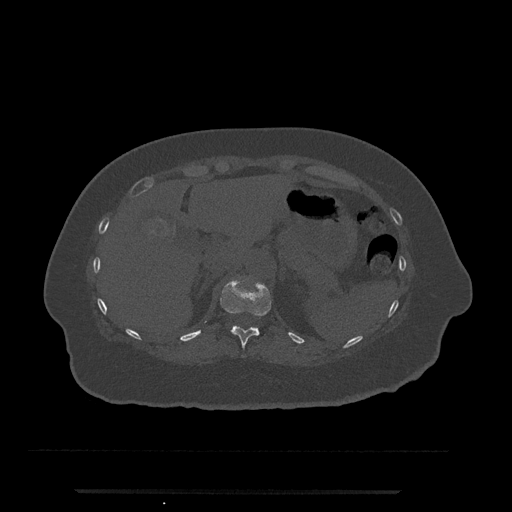
CT including the spine, one axial slice. Slice 218 of 797 in the series (ordered by position). Reconstruction kernel Br40s/3. Bone window (W 1800 / L 400 HU). 512 × 512 image matrix, field of view 440 × 440 mm. Female patient, age 51 years. From the clinical record (not read from this slice): primary cancer: neuro.
Outlined on this slice (semi-automatic segmentation, software-assisted and operator-edited):
- T11 vertebra: bounding box (x1, y1, x2, y2) in pixels: (220, 280, 271, 349)